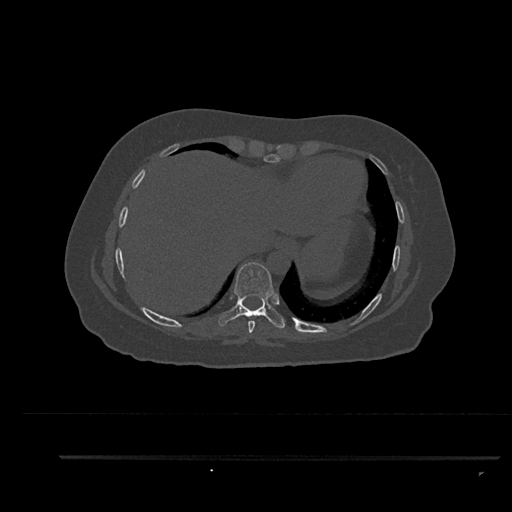
CT including the spine, one axial slice; slice 423 of 797 in the series (ordered by position); reconstruction kernel Br40s/3; 120 kVp; bone window (W 1800 / L 400 HU); 512 × 512 image matrix, field of view 408 × 408 mm. Patient: female, 44 years. Case-level facts recorded for this patient, not image findings: primary cancer: renal; vertebrae with lytic lesions (as recorded): L1.
Structures marked on this image (semi-automatically segmented with operator editing):
- T8 vertebra: bounding box <248,320,255,333> (left, top, right, bottom; pixels)
- T9 vertebra: <218,262,285,329>